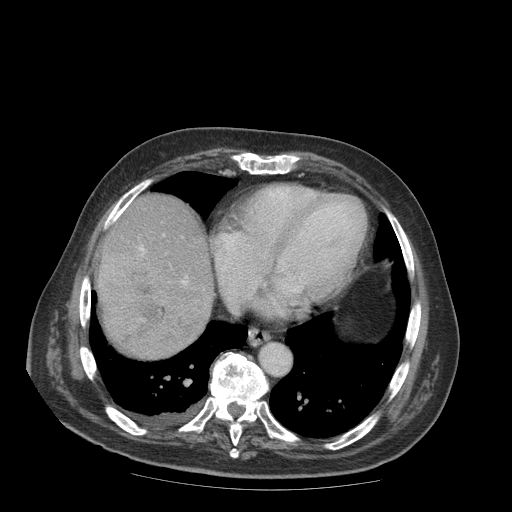
Contrast-enhanced abdominal CT (liver protocol), one axial slice. Position 83 of 99 along the scan axis. 140 kVp. Soft-tissue window (W 400 / L 40 HU). 512 × 512 image matrix. From the clinical record (not read from this slice): diagnosis: hepatocellular carcinoma (patient treated with transarterial chemoembolisation; whether this scan precedes or follows treatment is not stated here); TNM stage (as recorded): Stage-IIIB.
Annotated regions visible in this slice (semi-automatically segmented with operator editing):
- abdominal aorta: bounding box (x1, y1, x2, y2) in pixels: (259, 342, 291, 375)
- liver parenchyma outside the tumour (the mass and vessels are separate outlines, so this box may not span the whole liver): (98, 194, 212, 313)
- mass: (95, 241, 209, 359)
- liver vessels: (139, 246, 188, 285)